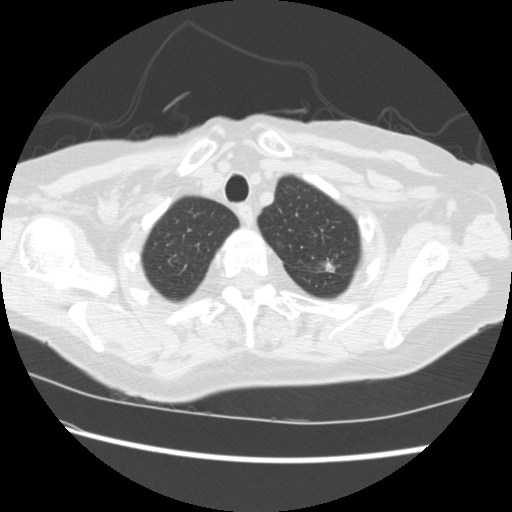
Low-dose screening chest CT, one axial slice; slice 192 of 224 in the series (ordered by position); lung window (W 1500 / L -600 HU); 512 × 512 image matrix.
Outlined on this slice (manually delineated by an expert):
- lesion 1 (tumor, upper lobe of left lung): box from (x=325, y=262) to (x=335, y=272) px